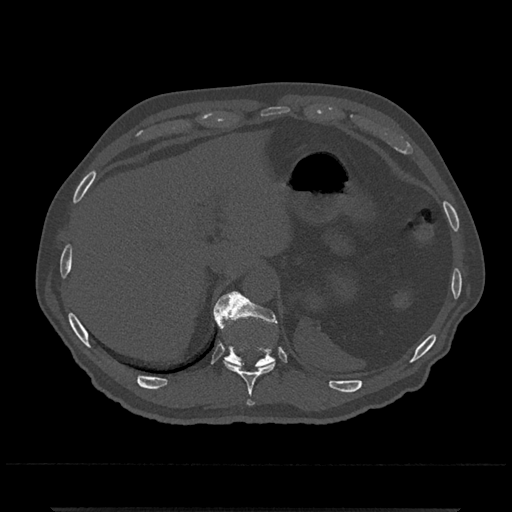
CT including the spine, one axial slice; reconstruction kernel Br40s/3; bone window (W 1800 / L 400 HU); 512 × 512 image matrix, field of view 393 × 393 mm. Patient: male, 67 years. Case-level facts recorded for this patient, not image findings: primary cancer: prostate.
Structures marked on this image (semi-automatically segmented with operator editing):
- T10 vertebra: bounding box [x1, y1, x2, y2] px = [219, 325, 276, 406]
- T11 vertebra: [213, 292, 278, 367]